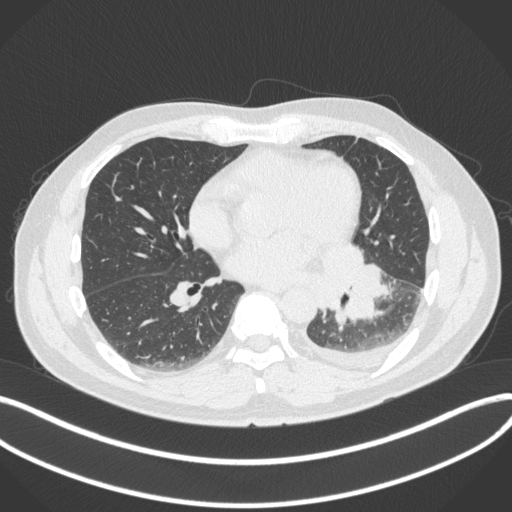
Chest CT, one axial slice. Reconstruction kernel B31f. Lung window (W 1500 / L -600 HU). 512 × 512 image matrix. Male patient, age 58 years. From the clinical record (not read from this slice): clinical TNM (as recorded): T3 N1 M1b.
Structures marked on this image (rectangle marked by the reading radiologist):
- lung tumour (recorded histology: small cell carcinoma): bounding box (x1, y1, x2, y2) in pixels: (315, 239, 386, 329)